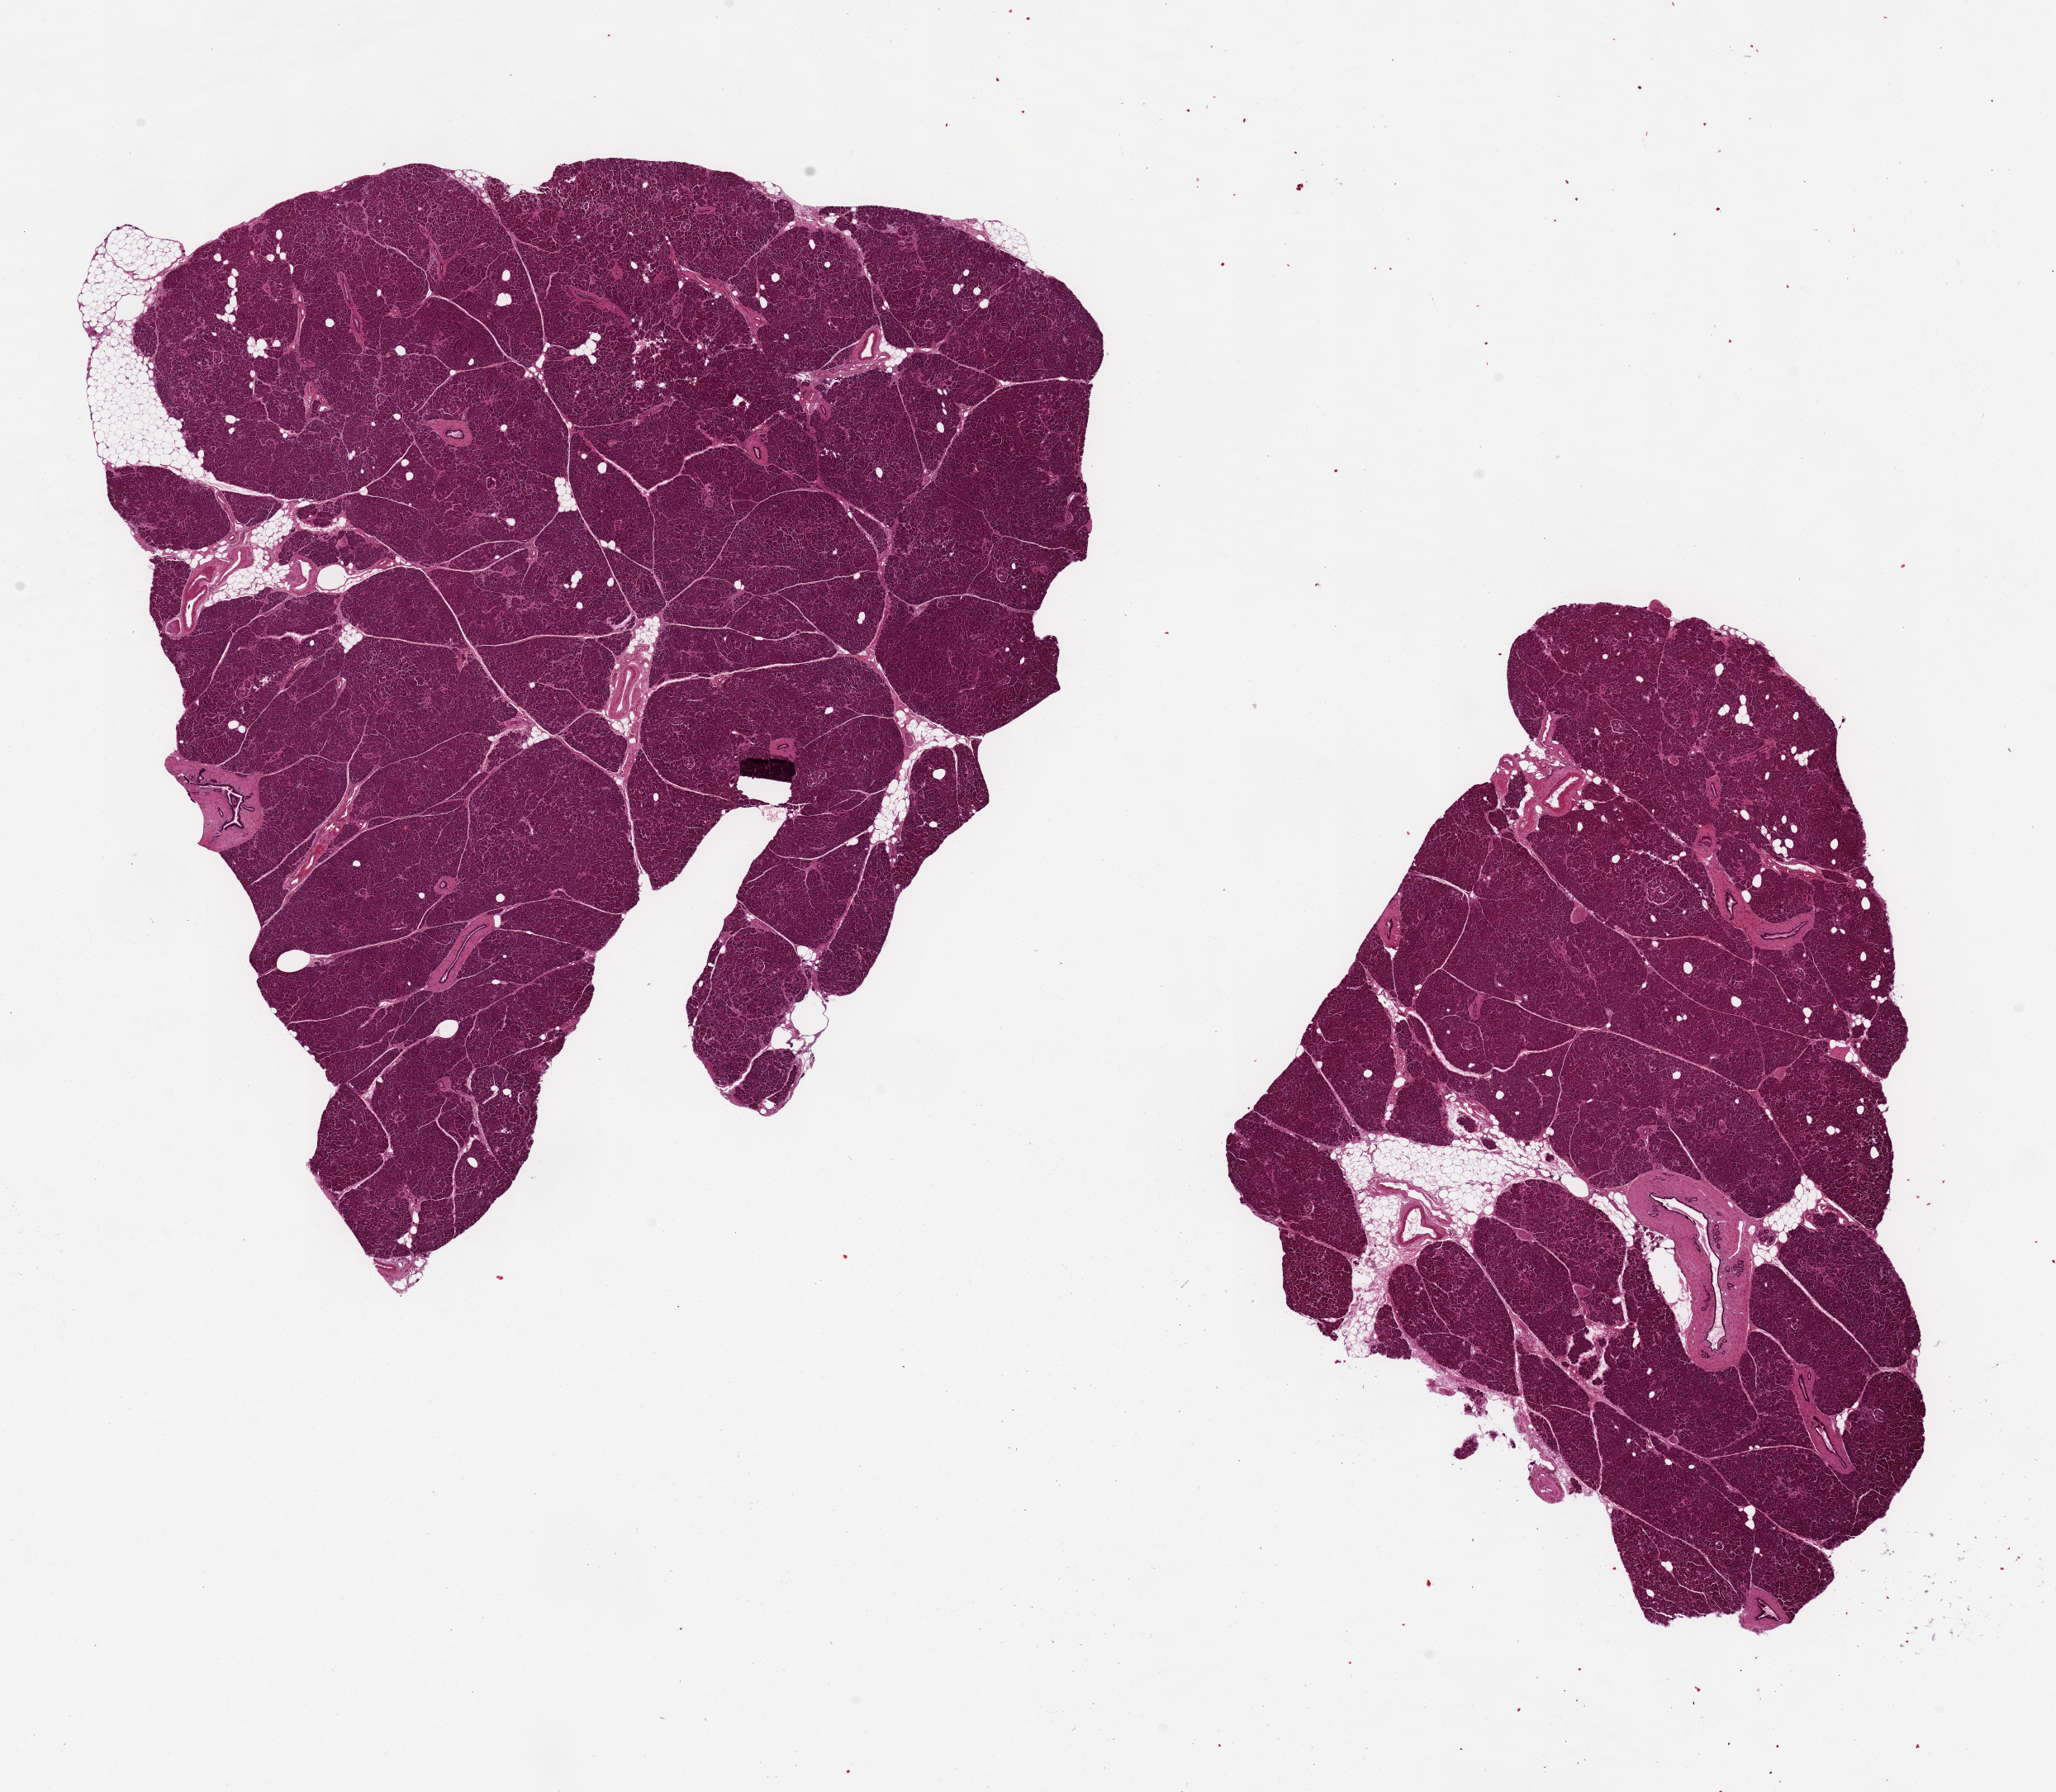
Haematoxylin and eosin whole-slide image, shown as a low-resolution overview of the whole scanned area (about 19.7 x 17.2 mm, slide scanned at 20x), PAXgene-fixed paraffin-embedded (PFPE) section, section of pancreas (target tissue), donor tissue sample. Donor: male.
Review note (as recorded): 2 aliquots, remarkably well-preserved, minimal adipose tissue.